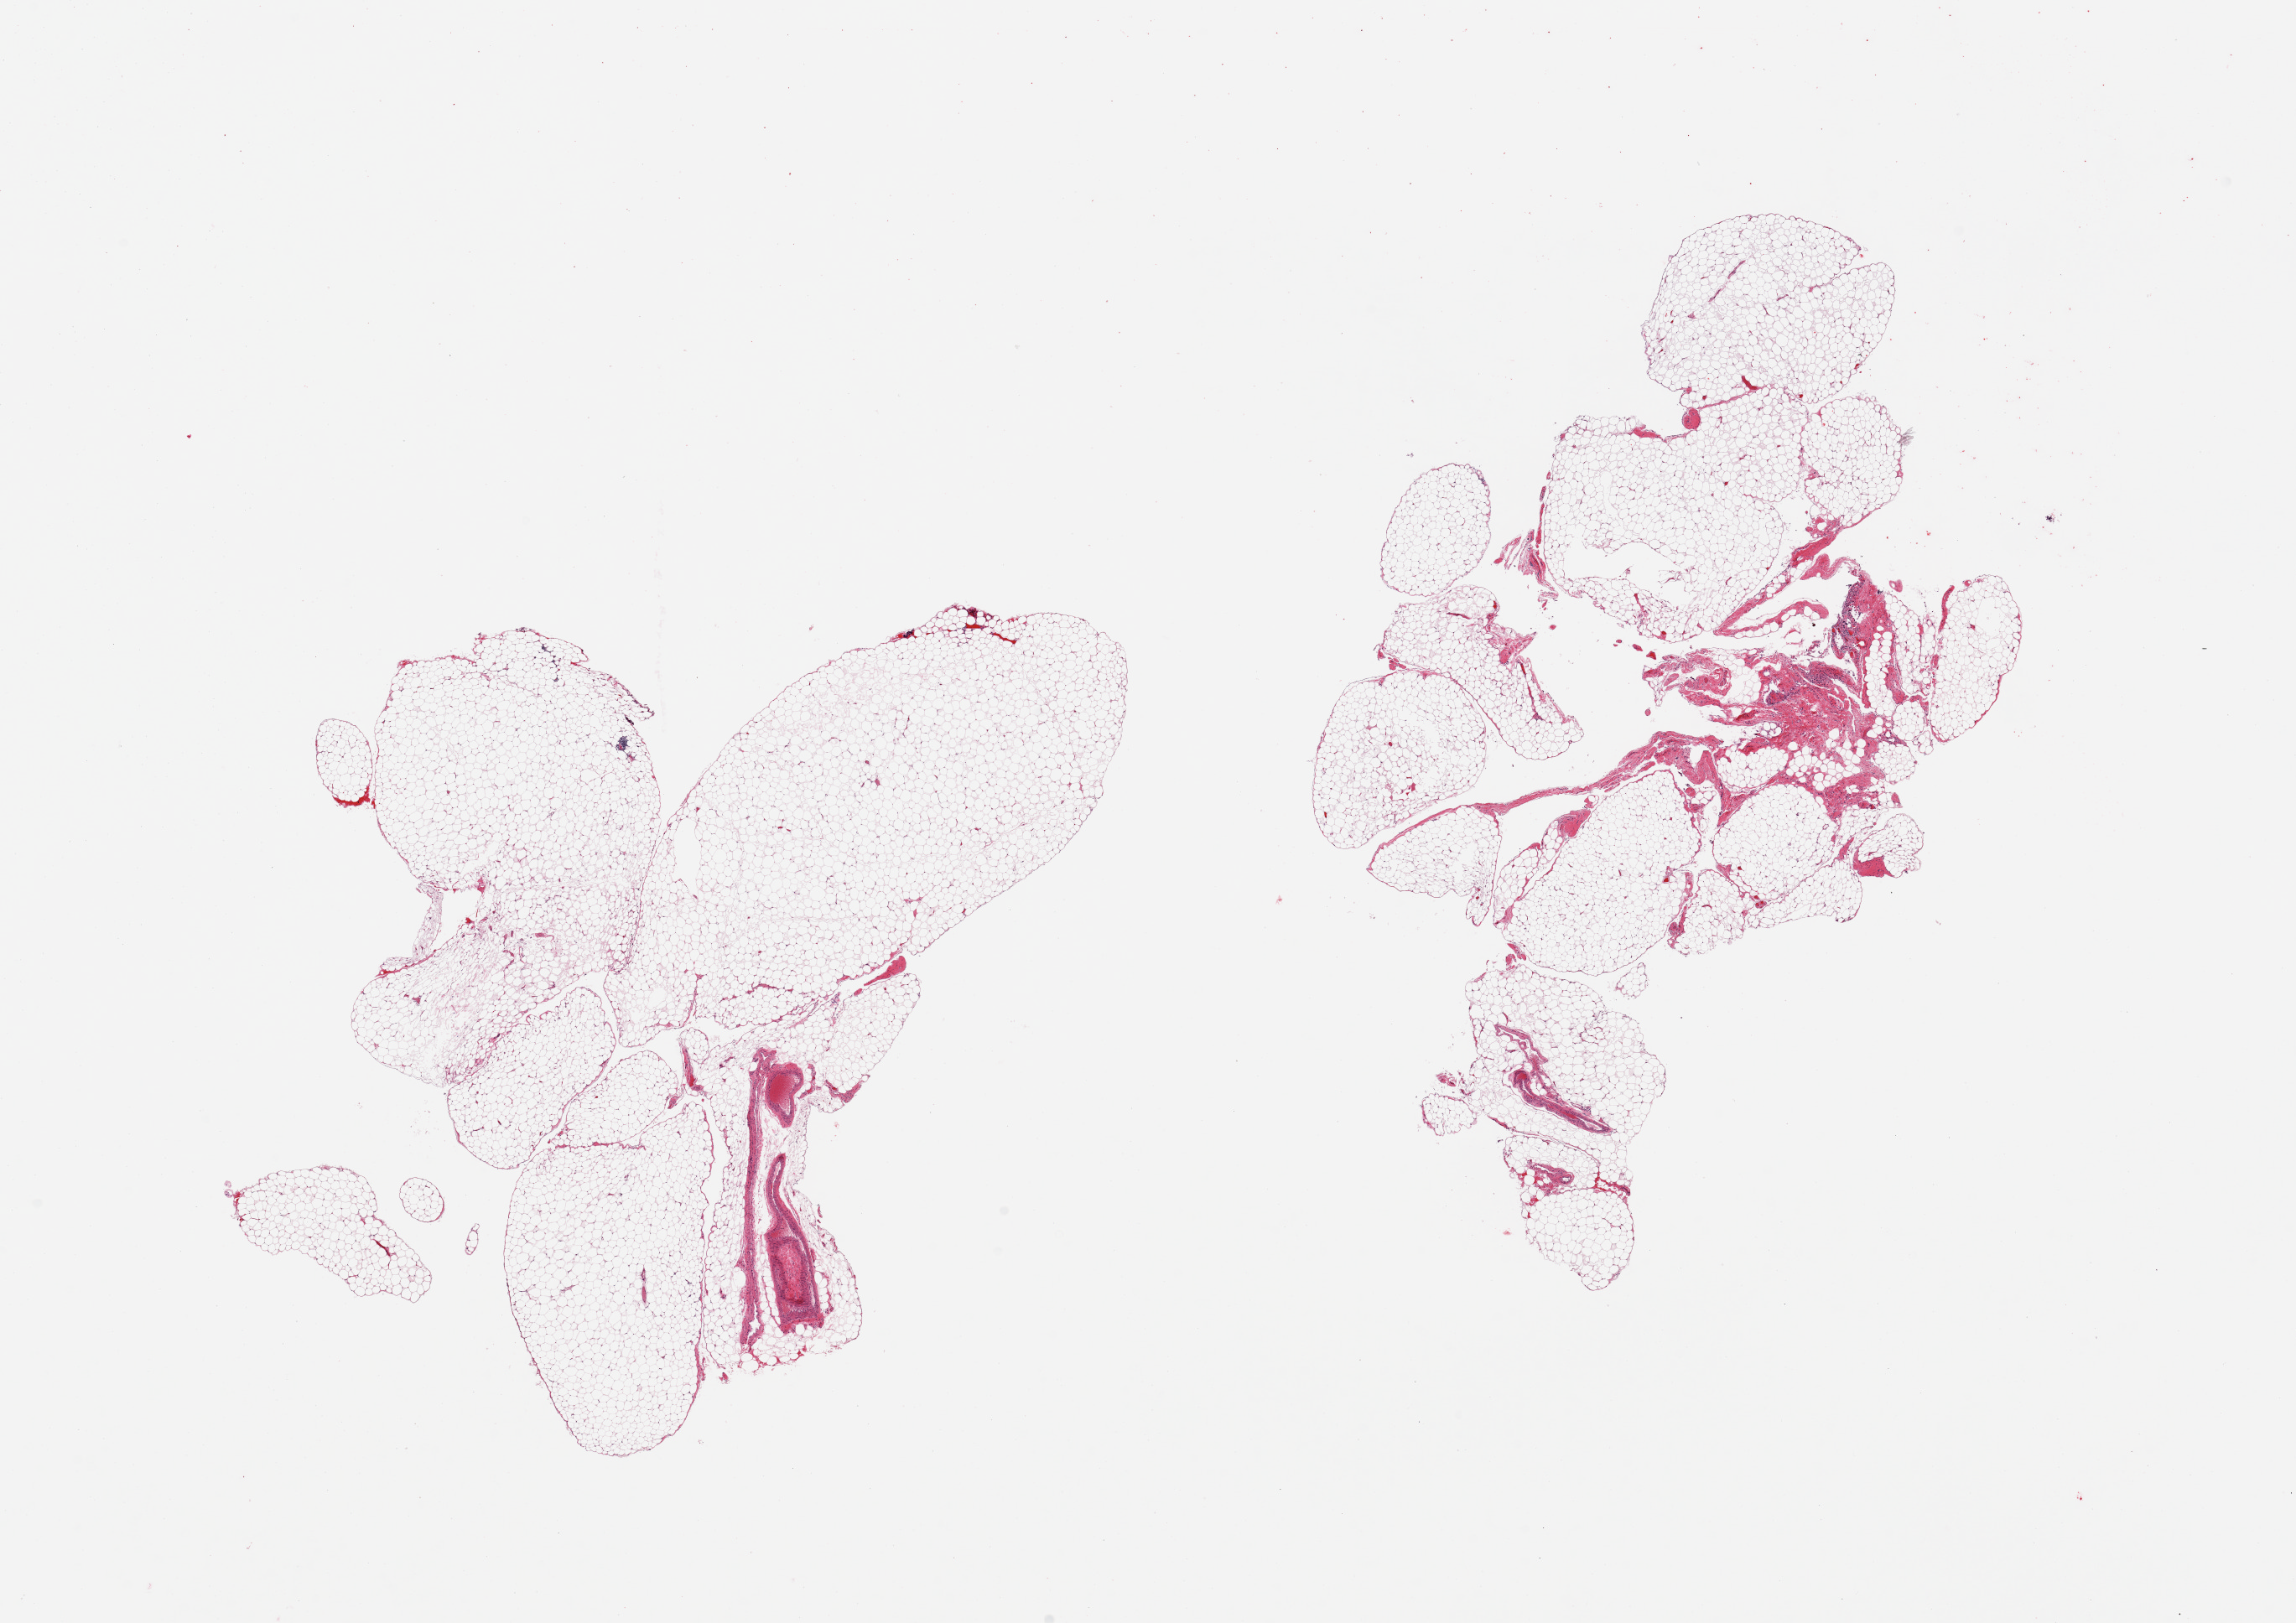
Digitized haematoxylin and eosin-stained section, whole scanned area (about 21.7 x 15.3 mm) shown as a low-resolution overview; PAXgene-fixed, paraffin-embedded tissue; sampled site (target tissue): omentum; donor tissue sample. Donor: female.
Reviewer comment on this tissue sample: 2 pieces; 5% fibrovascular content.